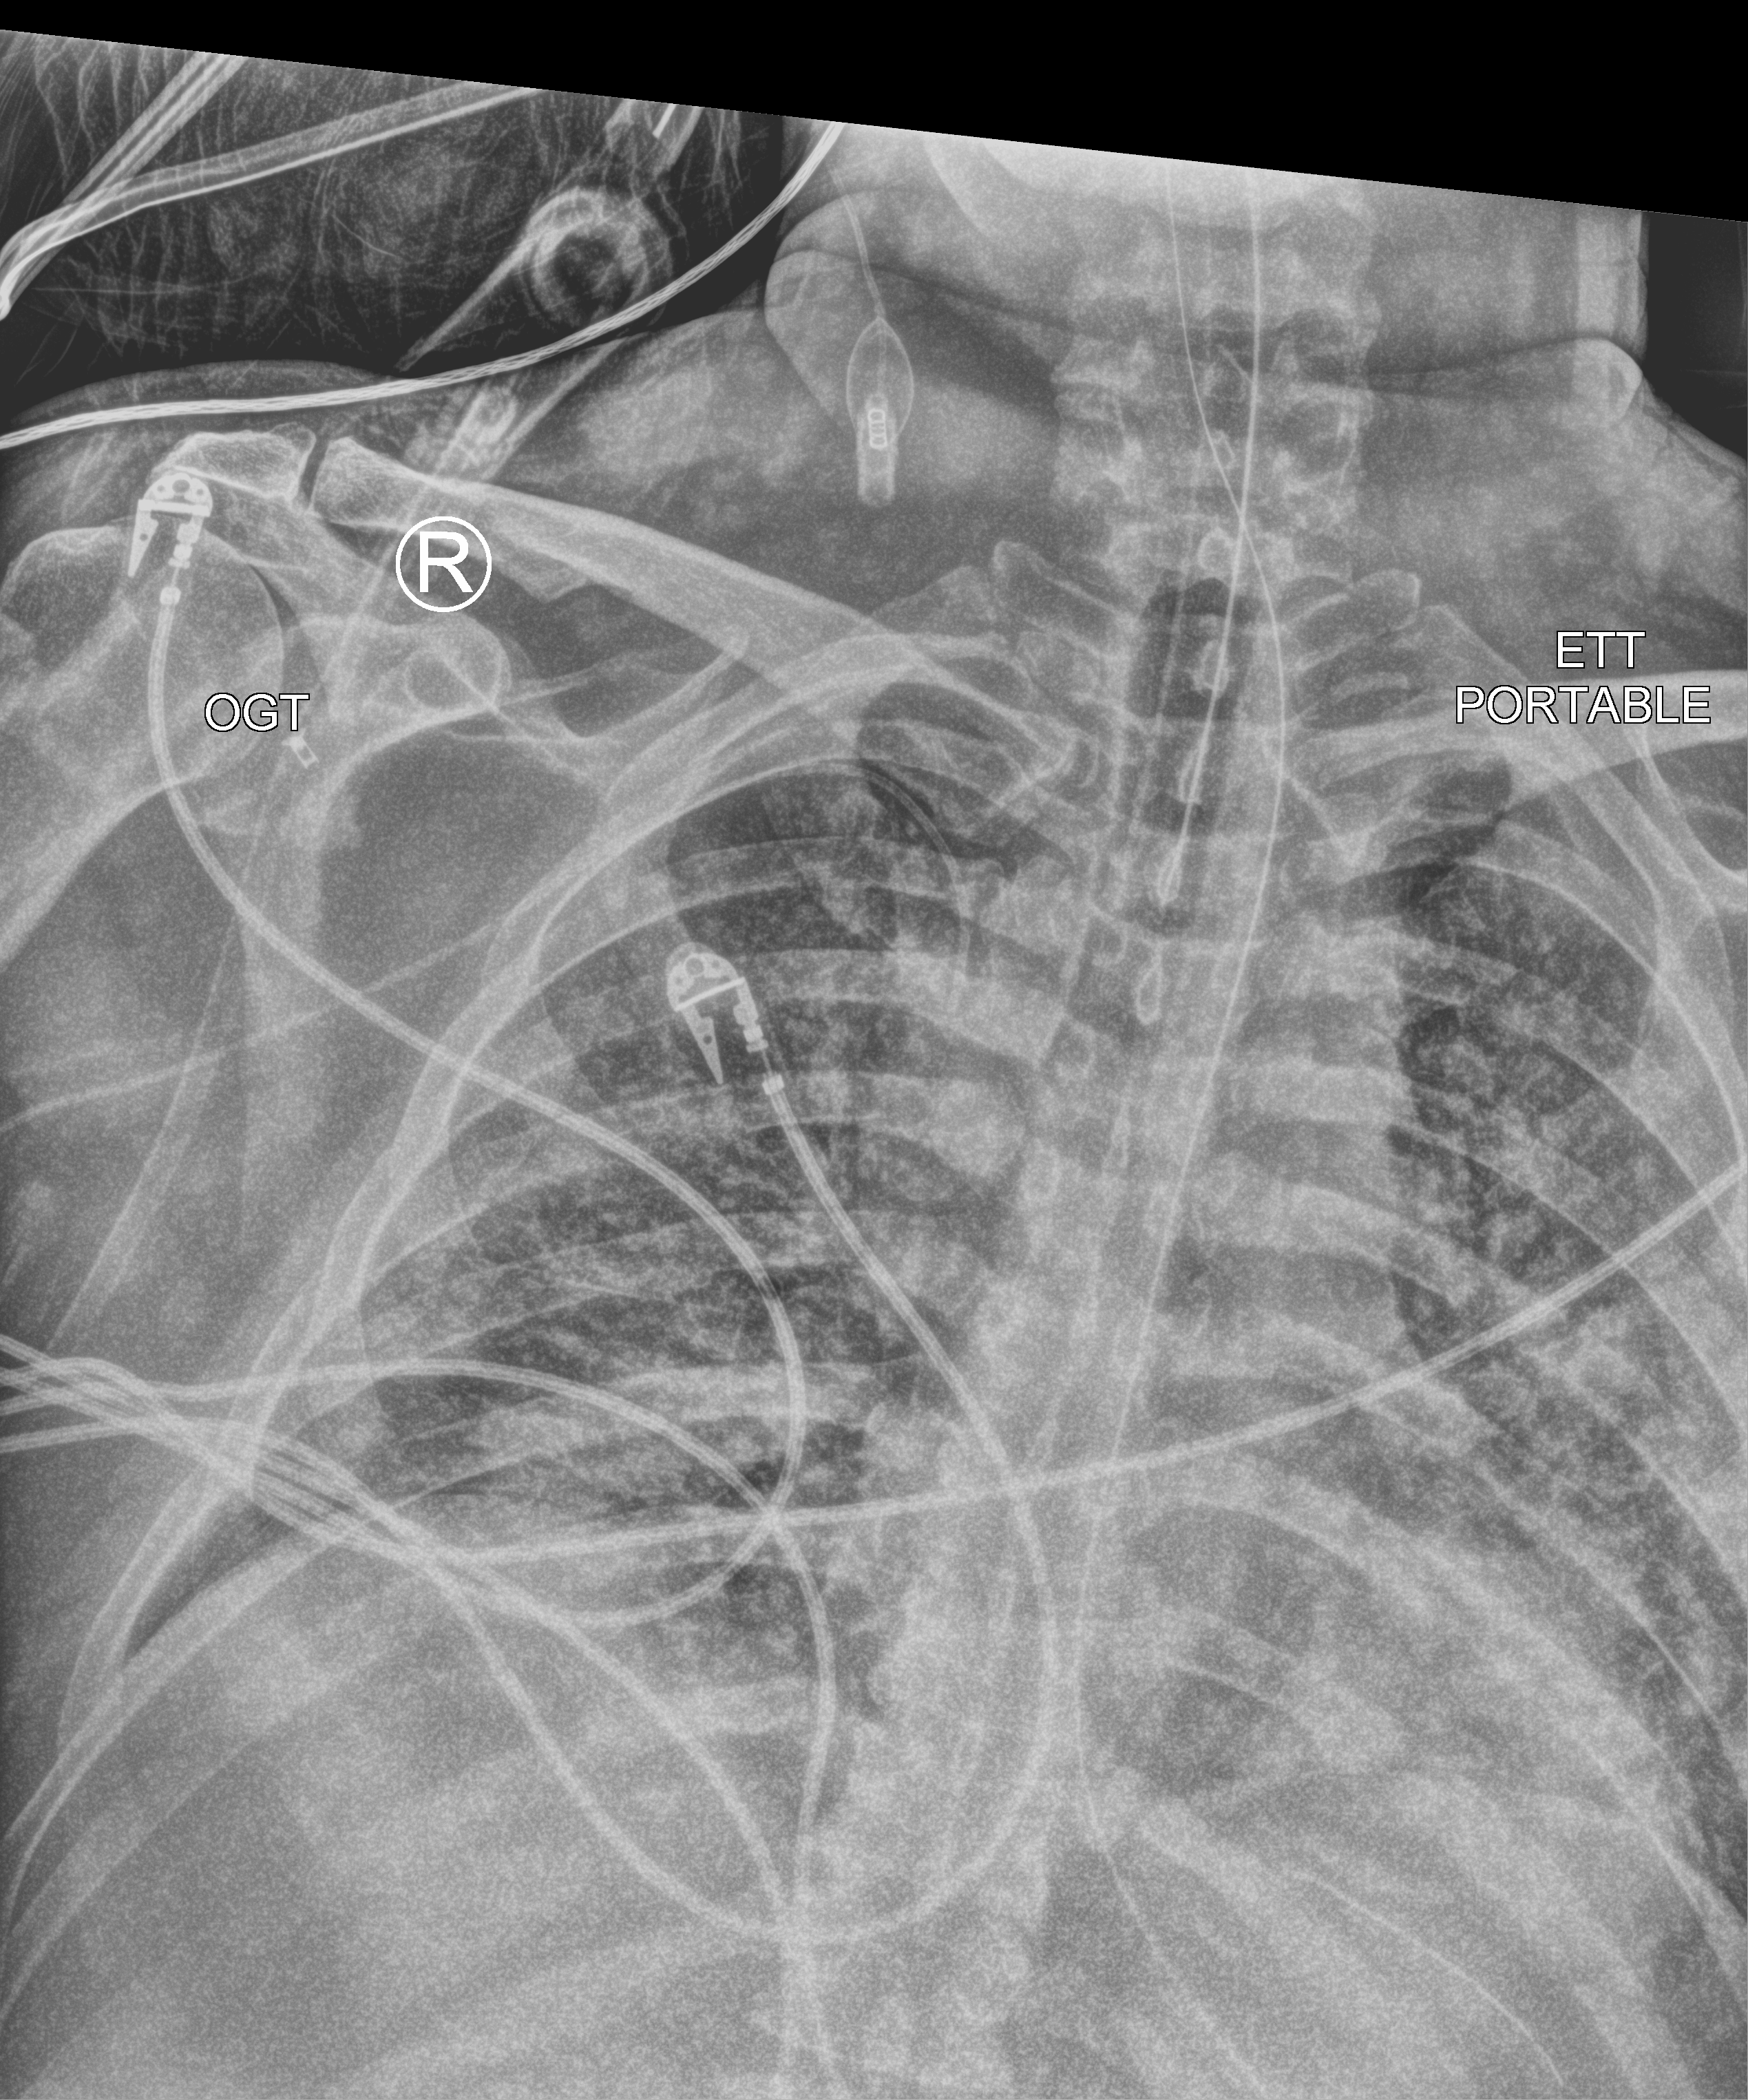
Portable chest radiograph, anteroposterior (AP) projection. Patient hospitalised with COVID-19; male, aged 18–59 years.
From the hospital-stay record, not from the radiograph (when in the stay this image was taken is not recorded):
- length of hospital stay: 52 days